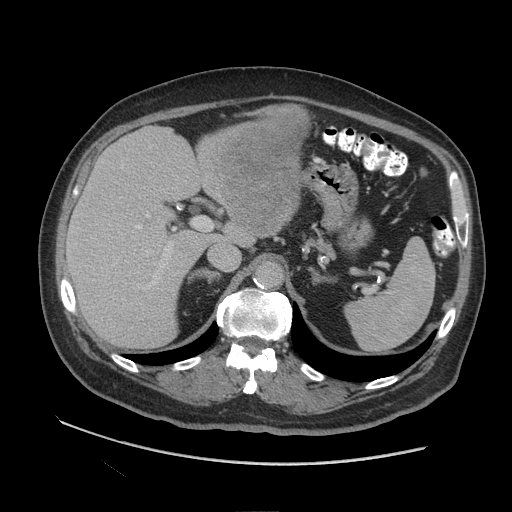
Contrast-enhanced abdominal CT (liver protocol), one axial slice. Slice 58 of 109 in the series (ordered by position). Soft-tissue window (W 400 / L 40 HU). 2.5 mm slice thickness. 512 × 512 image matrix, field of view 420 × 420 mm. From the clinical record (not read from this slice): diagnosis: hepatocellular carcinoma (patient treated with transarterial chemoembolisation; whether this scan precedes or follows treatment is not stated here); TNM stage (as recorded): Stage-I; Child-Pugh class: A; tumour nodularity: uninodular.
Annotated regions visible in this slice (semi-automatic segmentation, software-assisted and operator-edited):
- liver parenchyma outside the tumour (the mass and vessels are separate outlines, so this box may not span the whole liver): bounding box (x1, y1, x2, y2) in pixels: (66, 120, 258, 348)
- mass: (209, 104, 309, 236)
- liver vessels: (113, 214, 173, 299)